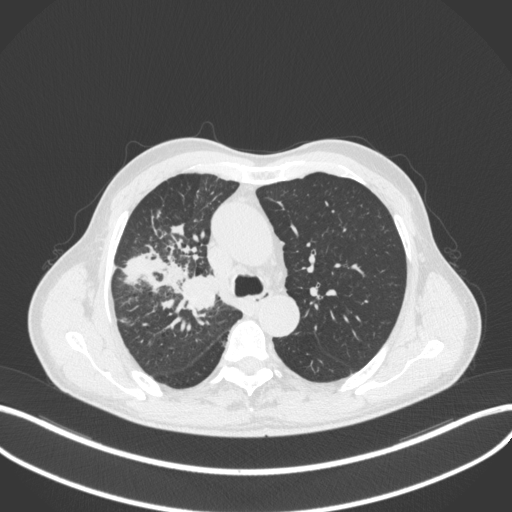
Chest CT, one axial slice; slice 333 of 490 in the series (ordered by position); reconstruction kernel B31f; 120 kVp; lung window (W 1500 / L -600 HU); 1 mm slice thickness; 512 × 512 image matrix, field of view 400 × 400 mm. Patient: male, 69 years. Case-level facts recorded for this patient, not image findings: clinical TNM (as recorded): T2a N0 M0.
Outlined on this slice (bounding box drawn by a radiologist):
- lung tumour (recorded histology: adenocarcinoma): bounding box <171,271,222,318> (left, top, right, bottom; pixels)